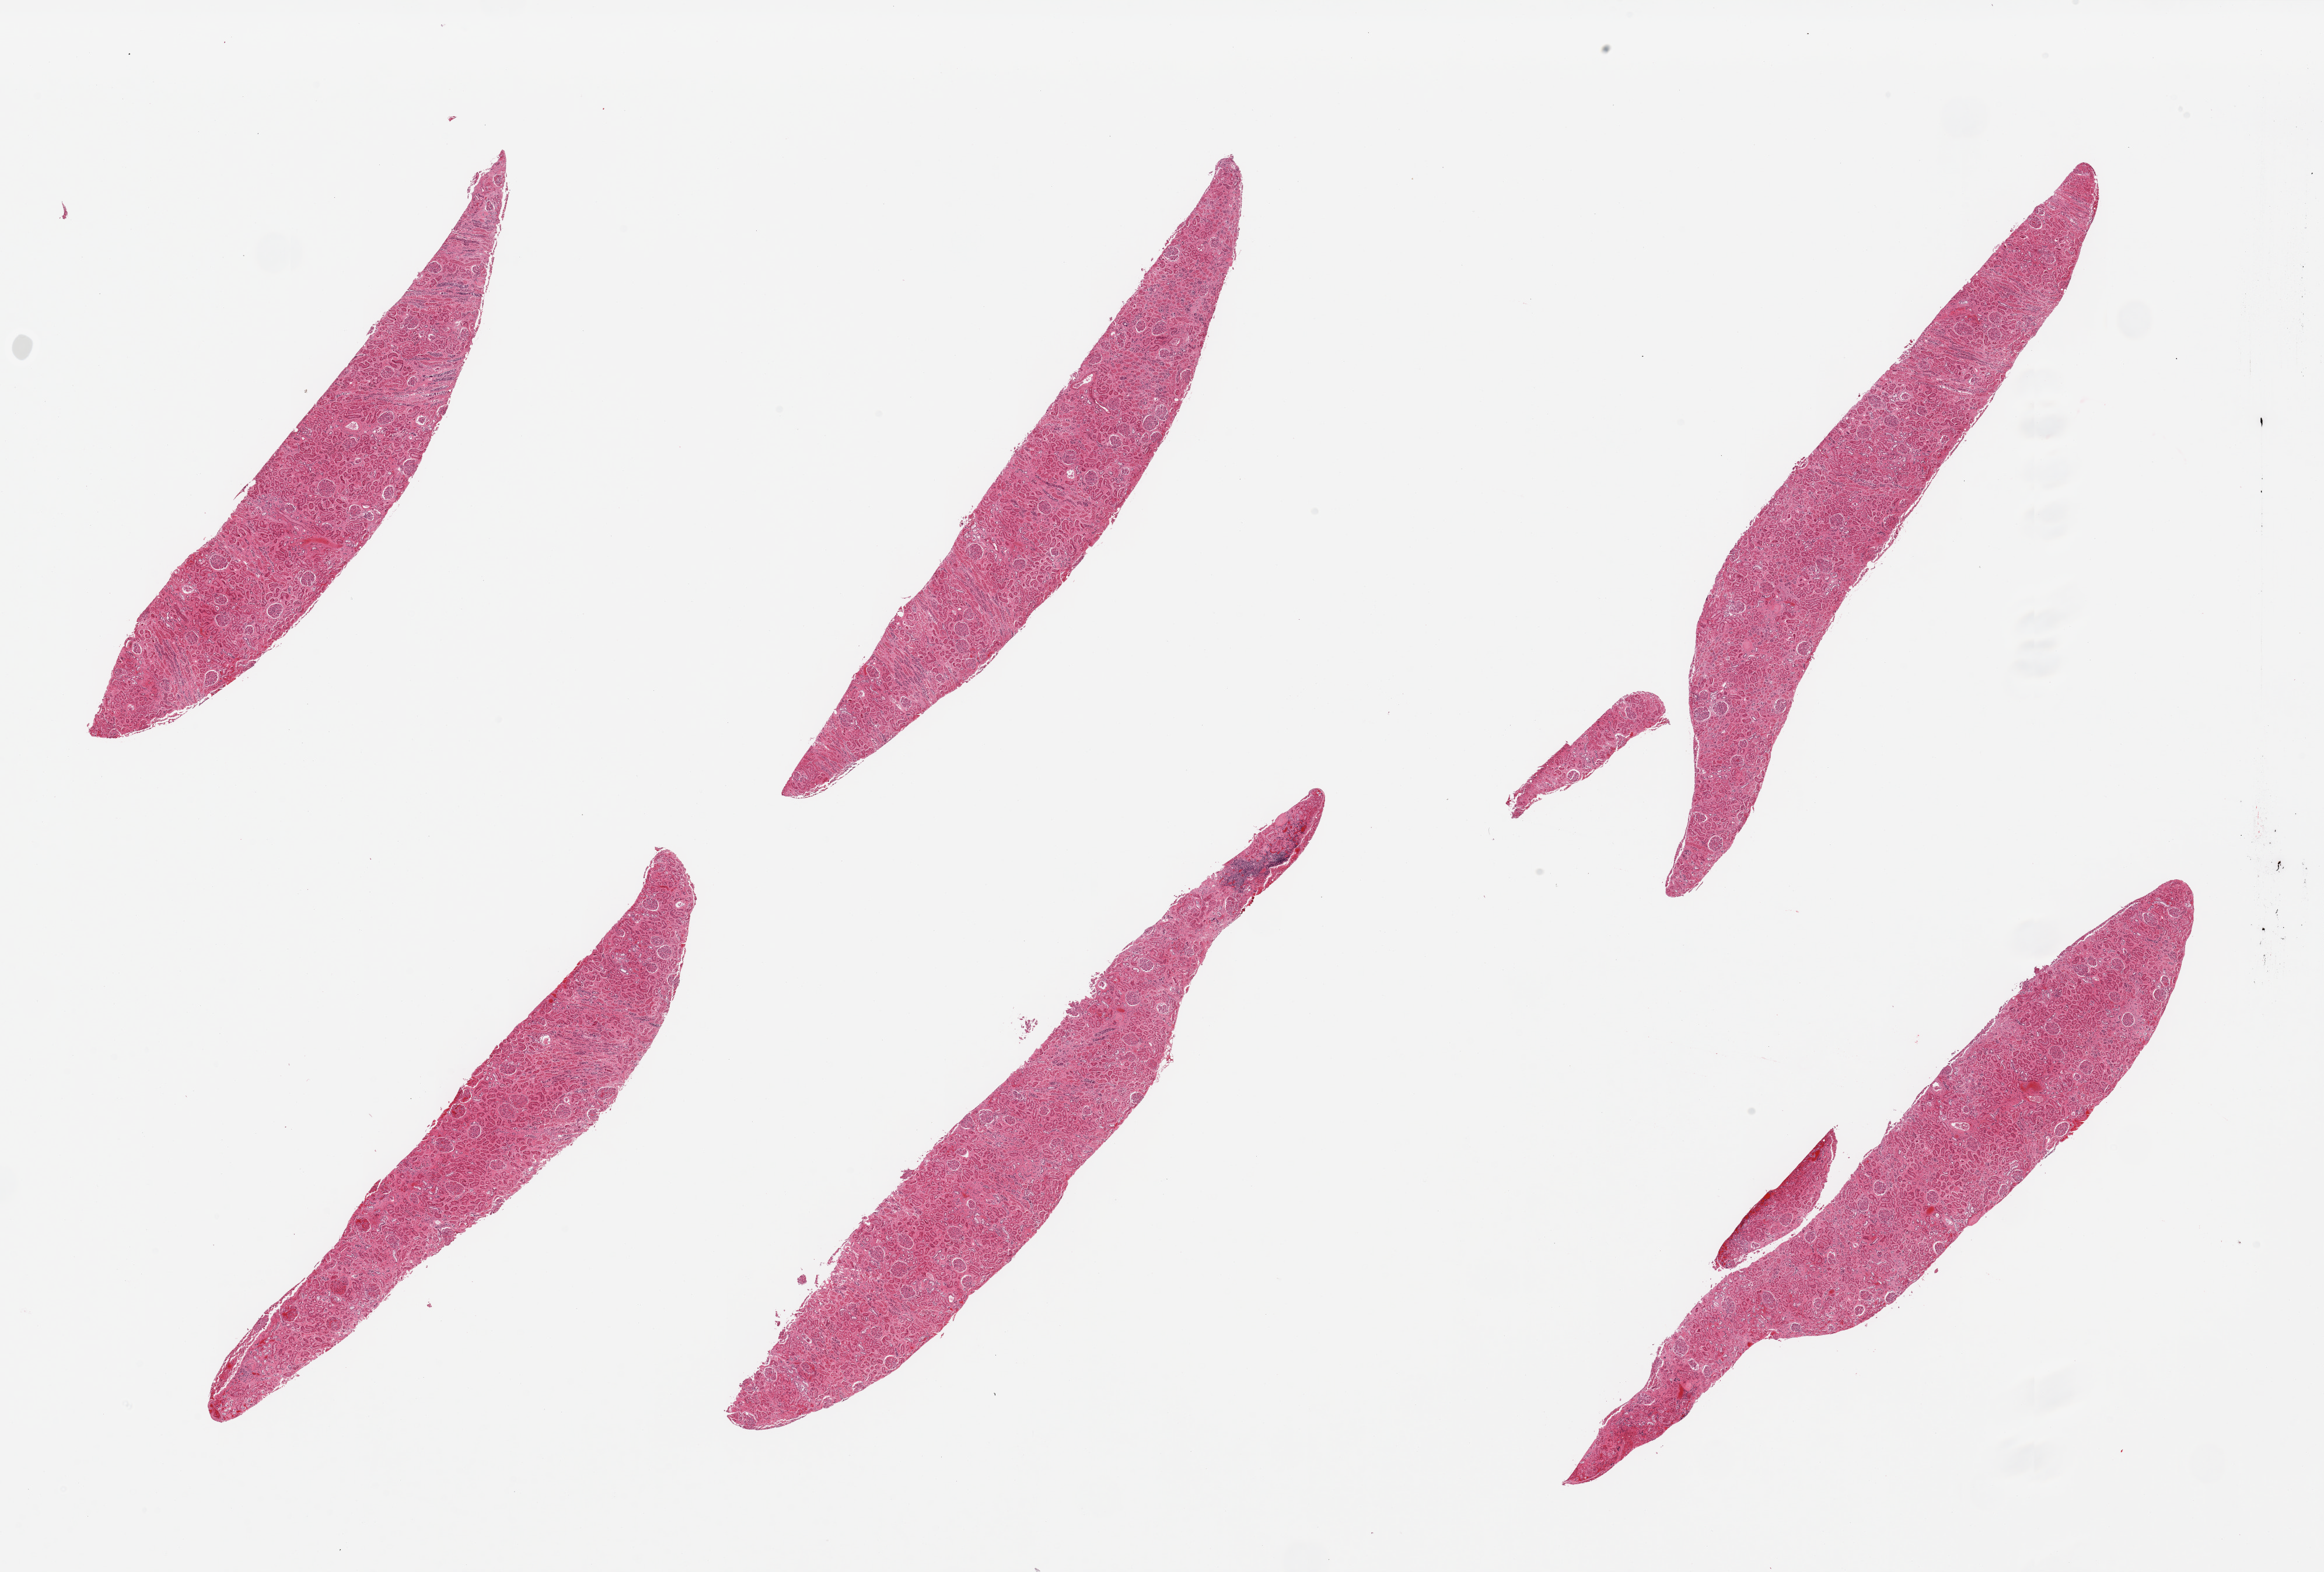
Hematoxylin and eosin (H&E) whole-slide image, brightfield — a low-resolution overview of the entire scanned area, about 31.5 x 21.3 mm, PAXgene-fixed paraffin-embedded (PFPE) section, section of renal cortex (target tissue), donor tissue sample. Donor sex: female.
Reviewer comment on this tissue sample: 6 pieces, glomeruli present; tubules less autolyzed than usual.